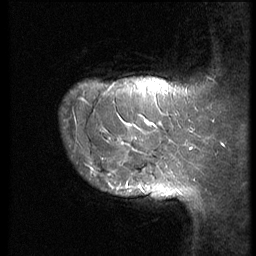
Breast MRI (dynamic contrast-enhanced), one sagittal slice; 3 images stored at this slice position (order not interpretable as contrast timing); 1.5 T; TE 4.2 ms, TR 9 ms; 2.5 mm slice thickness; 256 × 256 image matrix, field of view 180 × 180 mm. Patient: female, 28 years. From the clinical record (not read from this slice): setting: breast cancer imaged before/during neoadjuvant chemotherapy.
Outlined on this slice (semi-automatic segmentation, software-assisted and operator-edited):
- analysis volume of interest (the breast-tissue region the enhancement analysis was run in; not a lesion): box from (x=59, y=102) to (x=192, y=173) px
- tumour enhancement mask (voxels above the 140 % enhancement threshold inside the analysis volume of interest): (x=86, y=120)–(x=153, y=165)